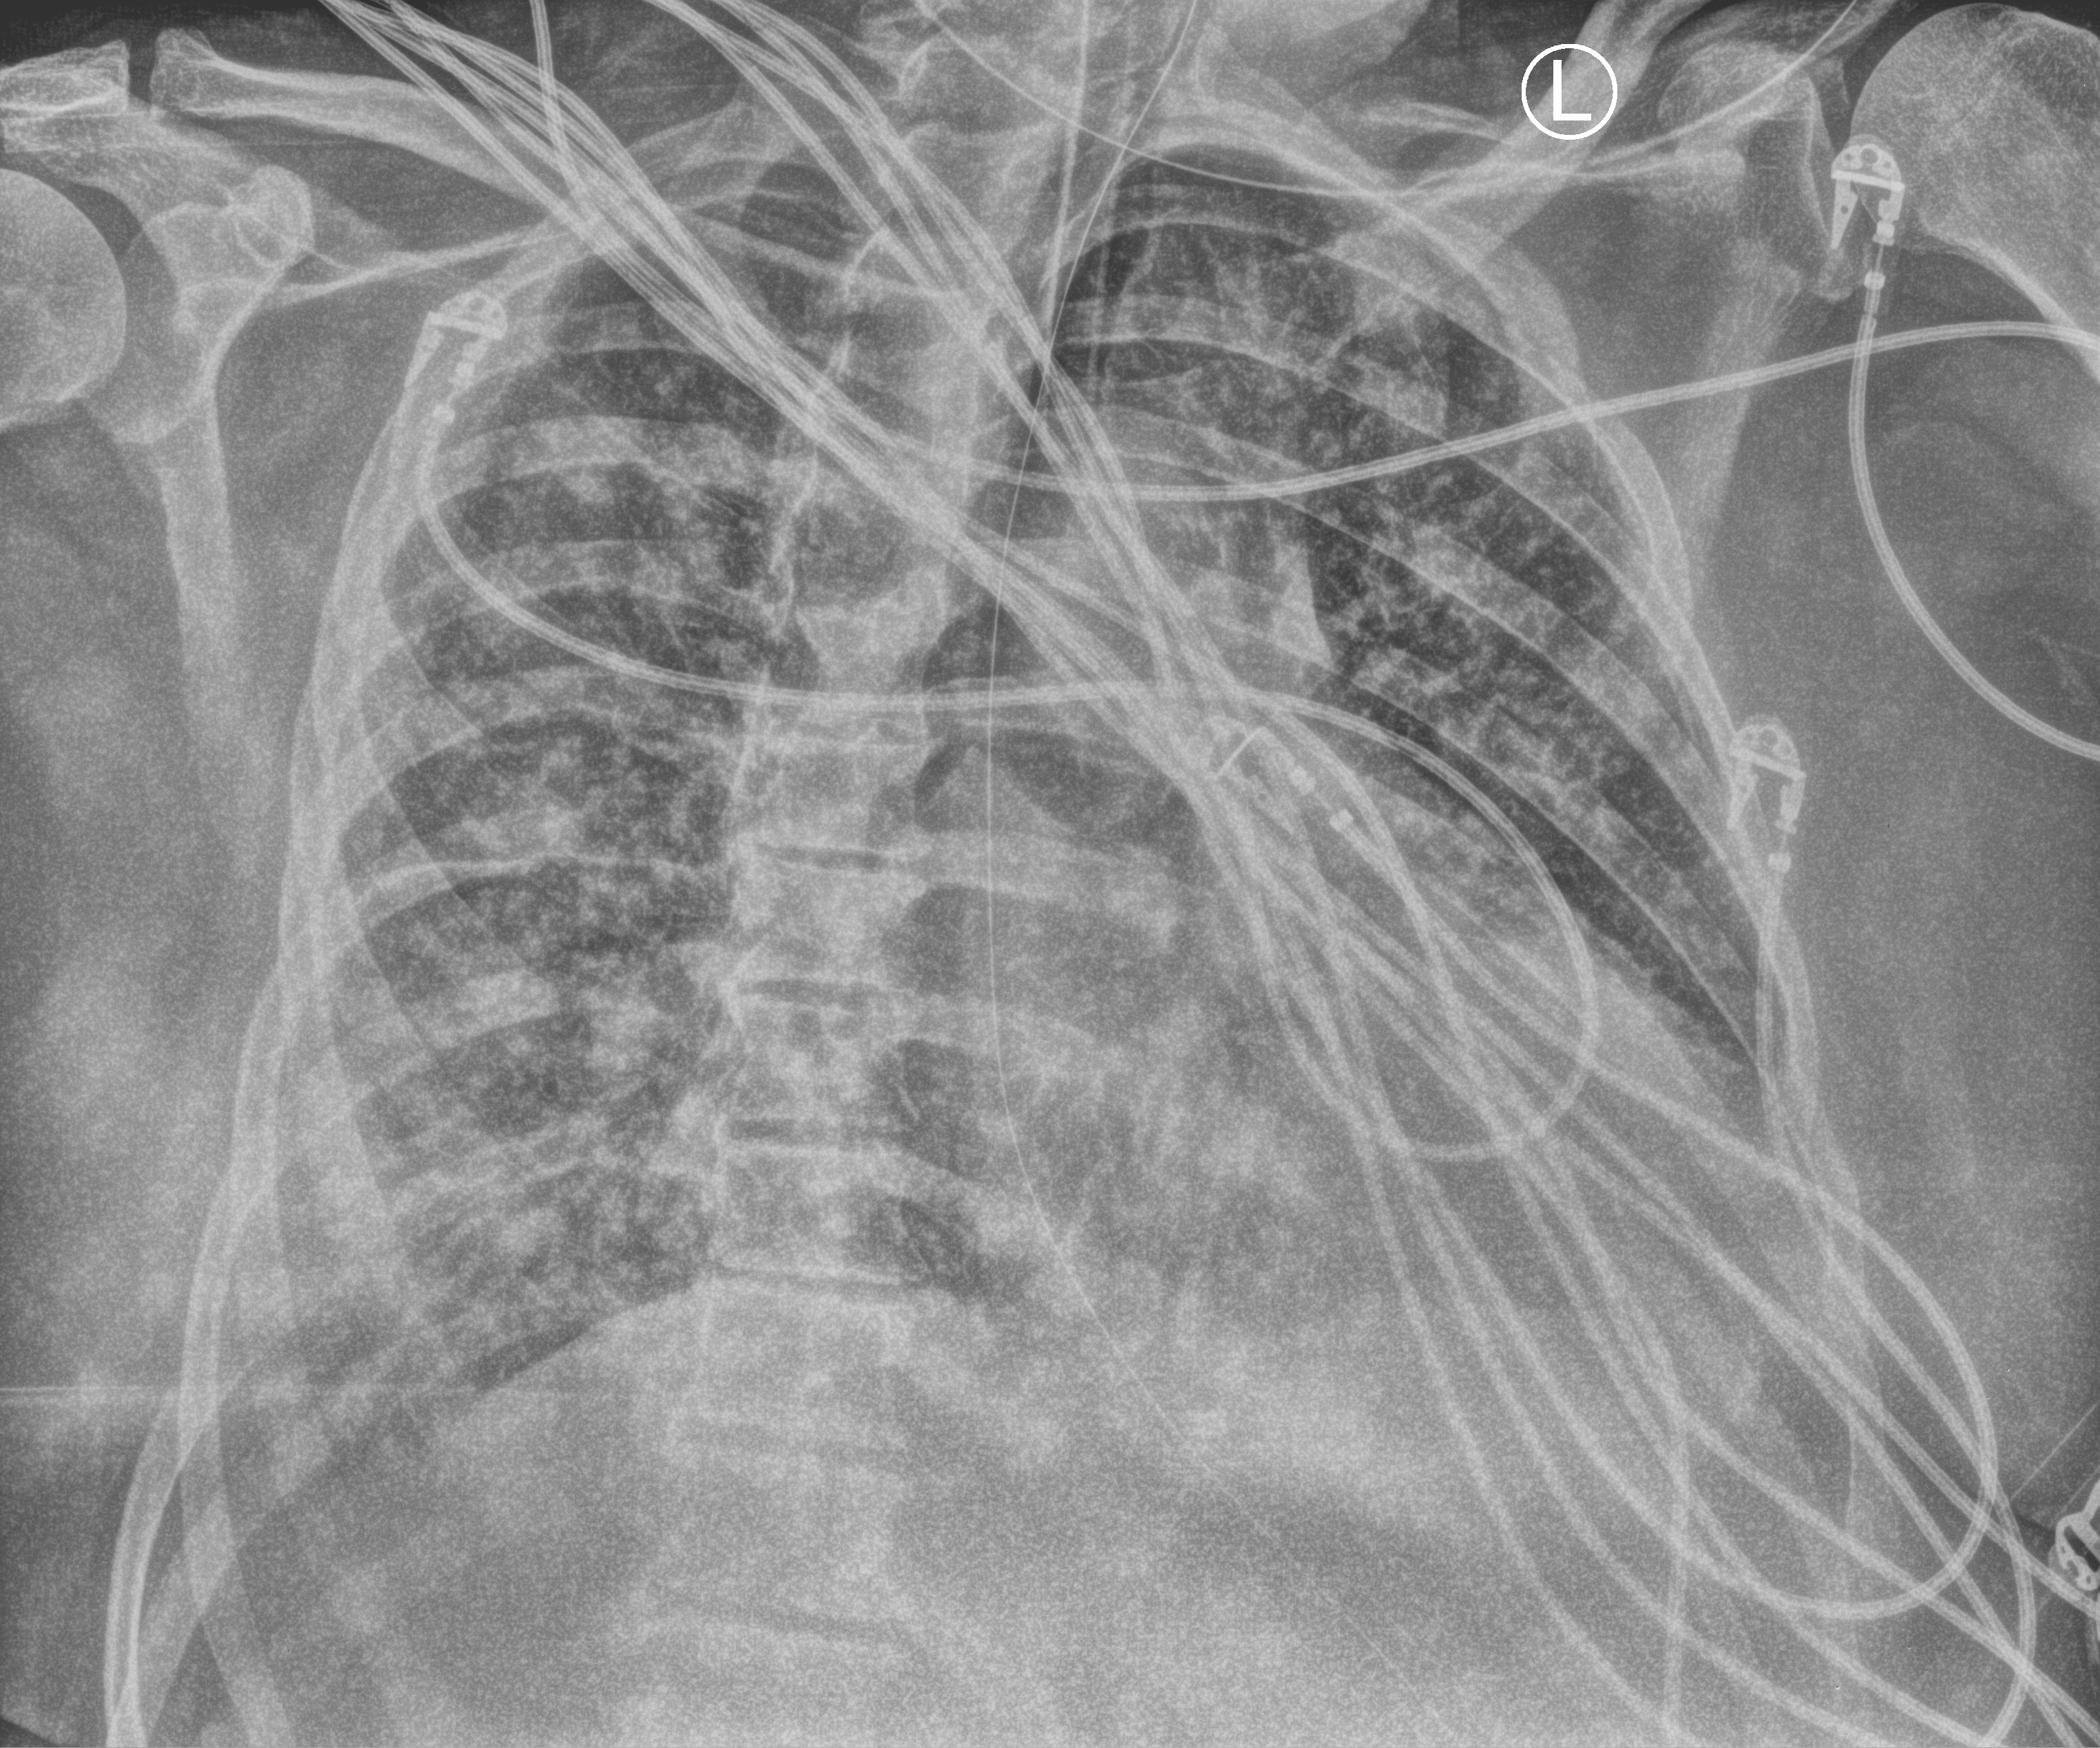
Bedside chest radiograph (computed radiography), anteroposterior (AP) projection. Patient hospitalised with COVID-19; male, aged 60–74 years.
Admission-level facts for this patient (not findings on this image; timing relative to this image not recorded): COPD (admission record): no; length of hospital stay: 40 days; chronic kidney disease (admission record): no.